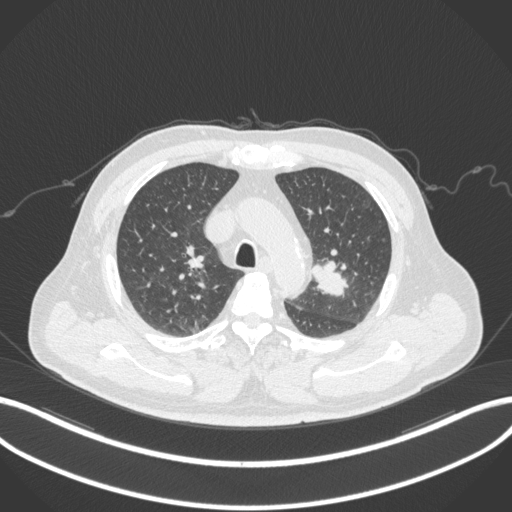
Chest CT, one axial slice. Position 222 of 286 along the scan axis. 120 kVp. Lung window (W 1500 / L -600 HU). 512 × 512 image matrix, field of view 400 × 400 mm. Male patient, age 67 years. From the clinical record (not read from this slice): clinical TNM (as recorded): T2a N1 M0; histopathological grade: G3.
Structures marked on this image (rectangle marked by the reading radiologist):
- lung tumour (recorded histology: adenocarcinoma): bounding box <312,258,350,301> (left, top, right, bottom; pixels)